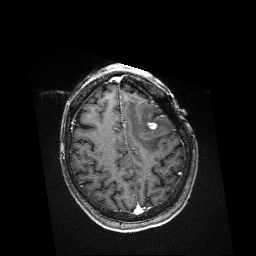
Brain MRI from a brain-tumour surgery series, one axial slice; slice 126 of 176 in the series (ordered by position); T1-weighted post-contrast; 1 mm slice thickness; 256 × 256 image matrix, field of view 256 × 256 mm. From the clinical record (not read from this slice): histopathology: Metastatic Melanoma; tumour location: Left Frontal.
Outlined on this slice (outlined manually by an expert reader):
- residual tumour: bounding box (x1, y1, x2, y2) in pixels: (148, 122, 157, 130)